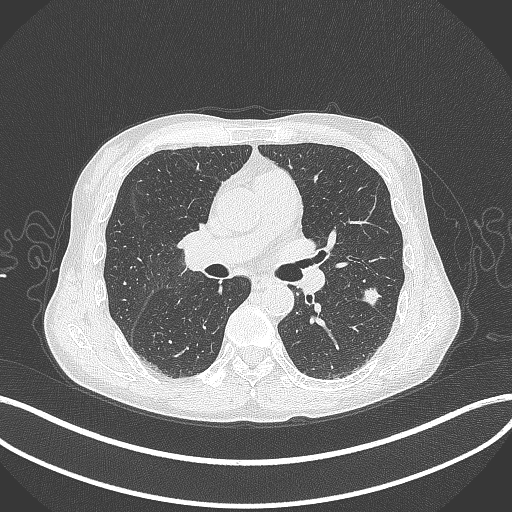
Chest CT, one axial slice. Position 203 of 429 along the scan axis. Reconstruction kernel B70f. Lung window (W 1500 / L -600 HU). 1 mm slice thickness. 512 × 512 image matrix. Patient: male, 58 years. From the clinical record (not read from this slice): clinical TNM (as recorded): T1c N0 M0; histopathological grade: G2.
Annotated regions visible in this slice (bounding box drawn by a radiologist):
- lung tumour (recorded histology: adenocarcinoma): bounding box (x1, y1, x2, y2) in pixels: (362, 283, 382, 307)